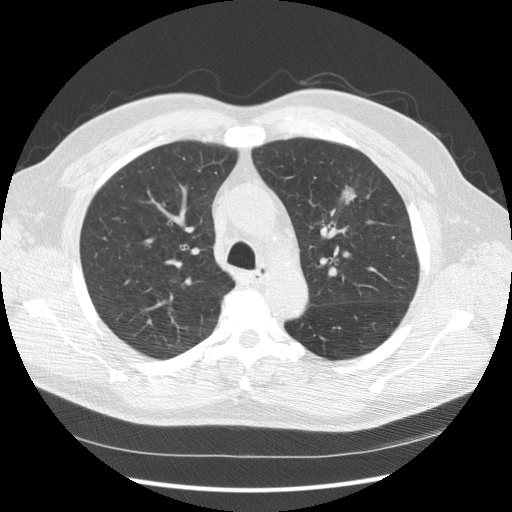
Chest CT (low-dose screening protocol), one axial image; second screening round (one year after baseline); lung window (W 1500 / L -600 HU); 120 kVp; slice 48 of 157 in the series. Male participant, aged 65 years at enrolment. Current smoker at enrolment.
Expert reader's lesion annotation, bounding box <327,175,373,221> (left, top, right, bottom; pixels). The screening reader recorded 2 non-calcified nodules or masses ≥4 mm on this exam (left upper lobe, right upper lobe); which of them this box marks is not recorded. Official screen result: positive, other.